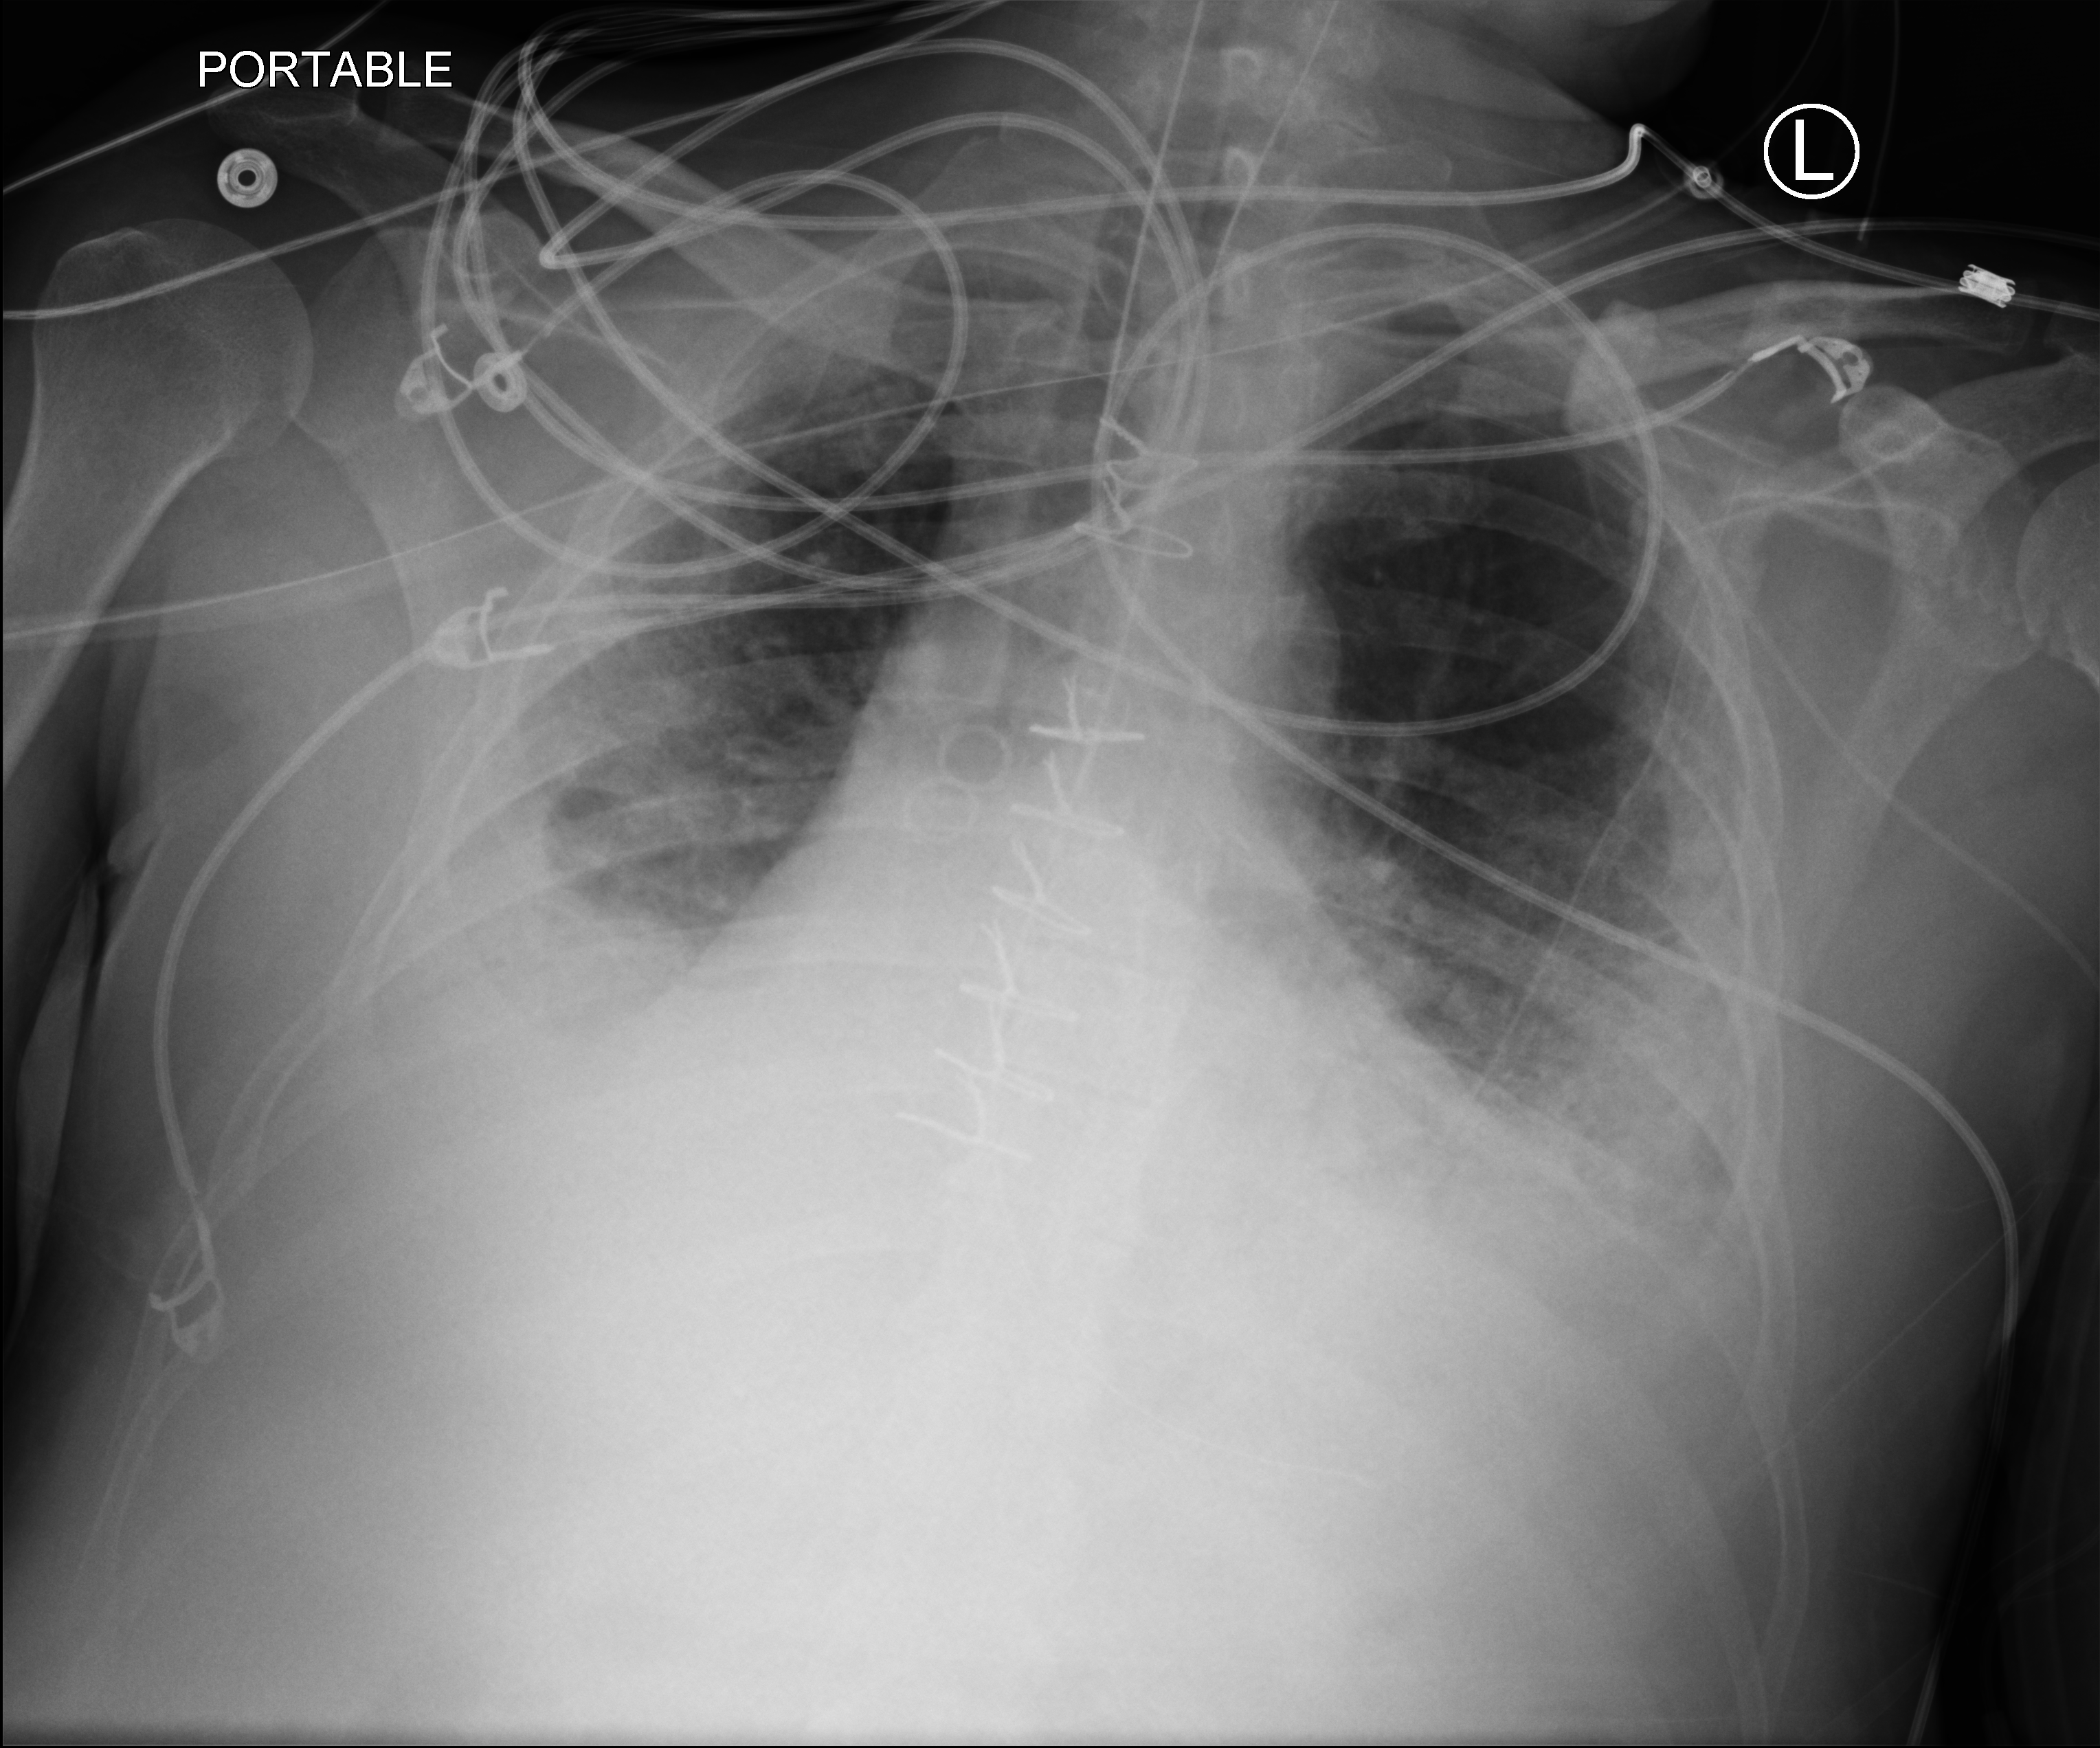
Chest X-ray (portable). Male patient hospitalised with COVID-19, age 18–59 years.
Hospital-stay facts (about this admission, not read from this image; timing relative to this image not recorded):
- mechanically ventilated during this hospital stay: yes
- admitted to intensive care during this hospital stay: yes
- chronic kidney disease (admission record): no